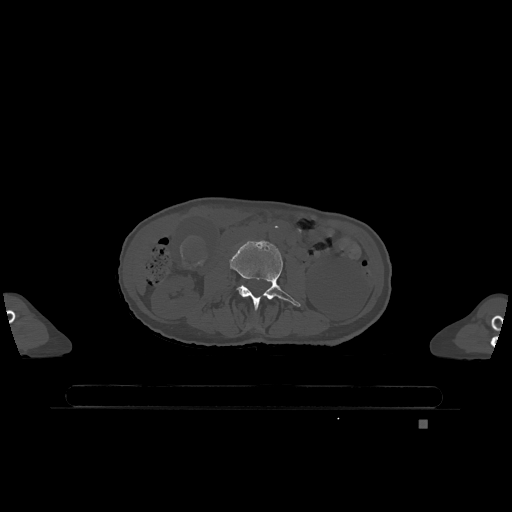
CT including the spine, one axial slice. Slice 356 of 1317 in the series (ordered by position). Bone window (W 1800 / L 400 HU). 0.5 mm slice thickness. 512 × 512 image matrix, field of view 500 × 500 mm. Patient: female, 74 years. From the clinical record (not read from this slice): primary cancer: lung; vertebrae with lytic lesions (as recorded): T1, T4, T5, T6, L4, L5.
Structures marked on this image (semi-automatic segmentation, software-assisted and operator-edited):
- L3 vertebra: bounding box <230,240,301,310> (left, top, right, bottom; pixels)